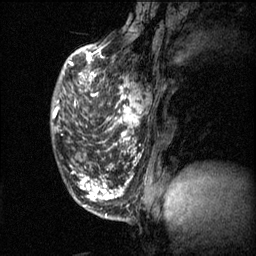
Breast MRI (dynamic contrast-enhanced), one sagittal slice. Slice 18 of 60 in the series (ordered by position). 3 images stored at this slice position (order not interpretable as contrast timing). 1.5 T. TE 4.2 ms, TR 11.1 ms. 256 × 256 image matrix, field of view 180 × 180 mm. Female patient, age 50 years.
Annotated regions visible in this slice (semi-automatic segmentation, software-assisted and operator-edited):
- analysis volume of interest (the breast-tissue region the enhancement analysis was run in; not a lesion): box from (x=78, y=68) to (x=153, y=141) px
- tumour enhancement mask (voxels above the 70 % enhancement threshold inside the analysis volume of interest): (x=78, y=70)–(x=143, y=141)